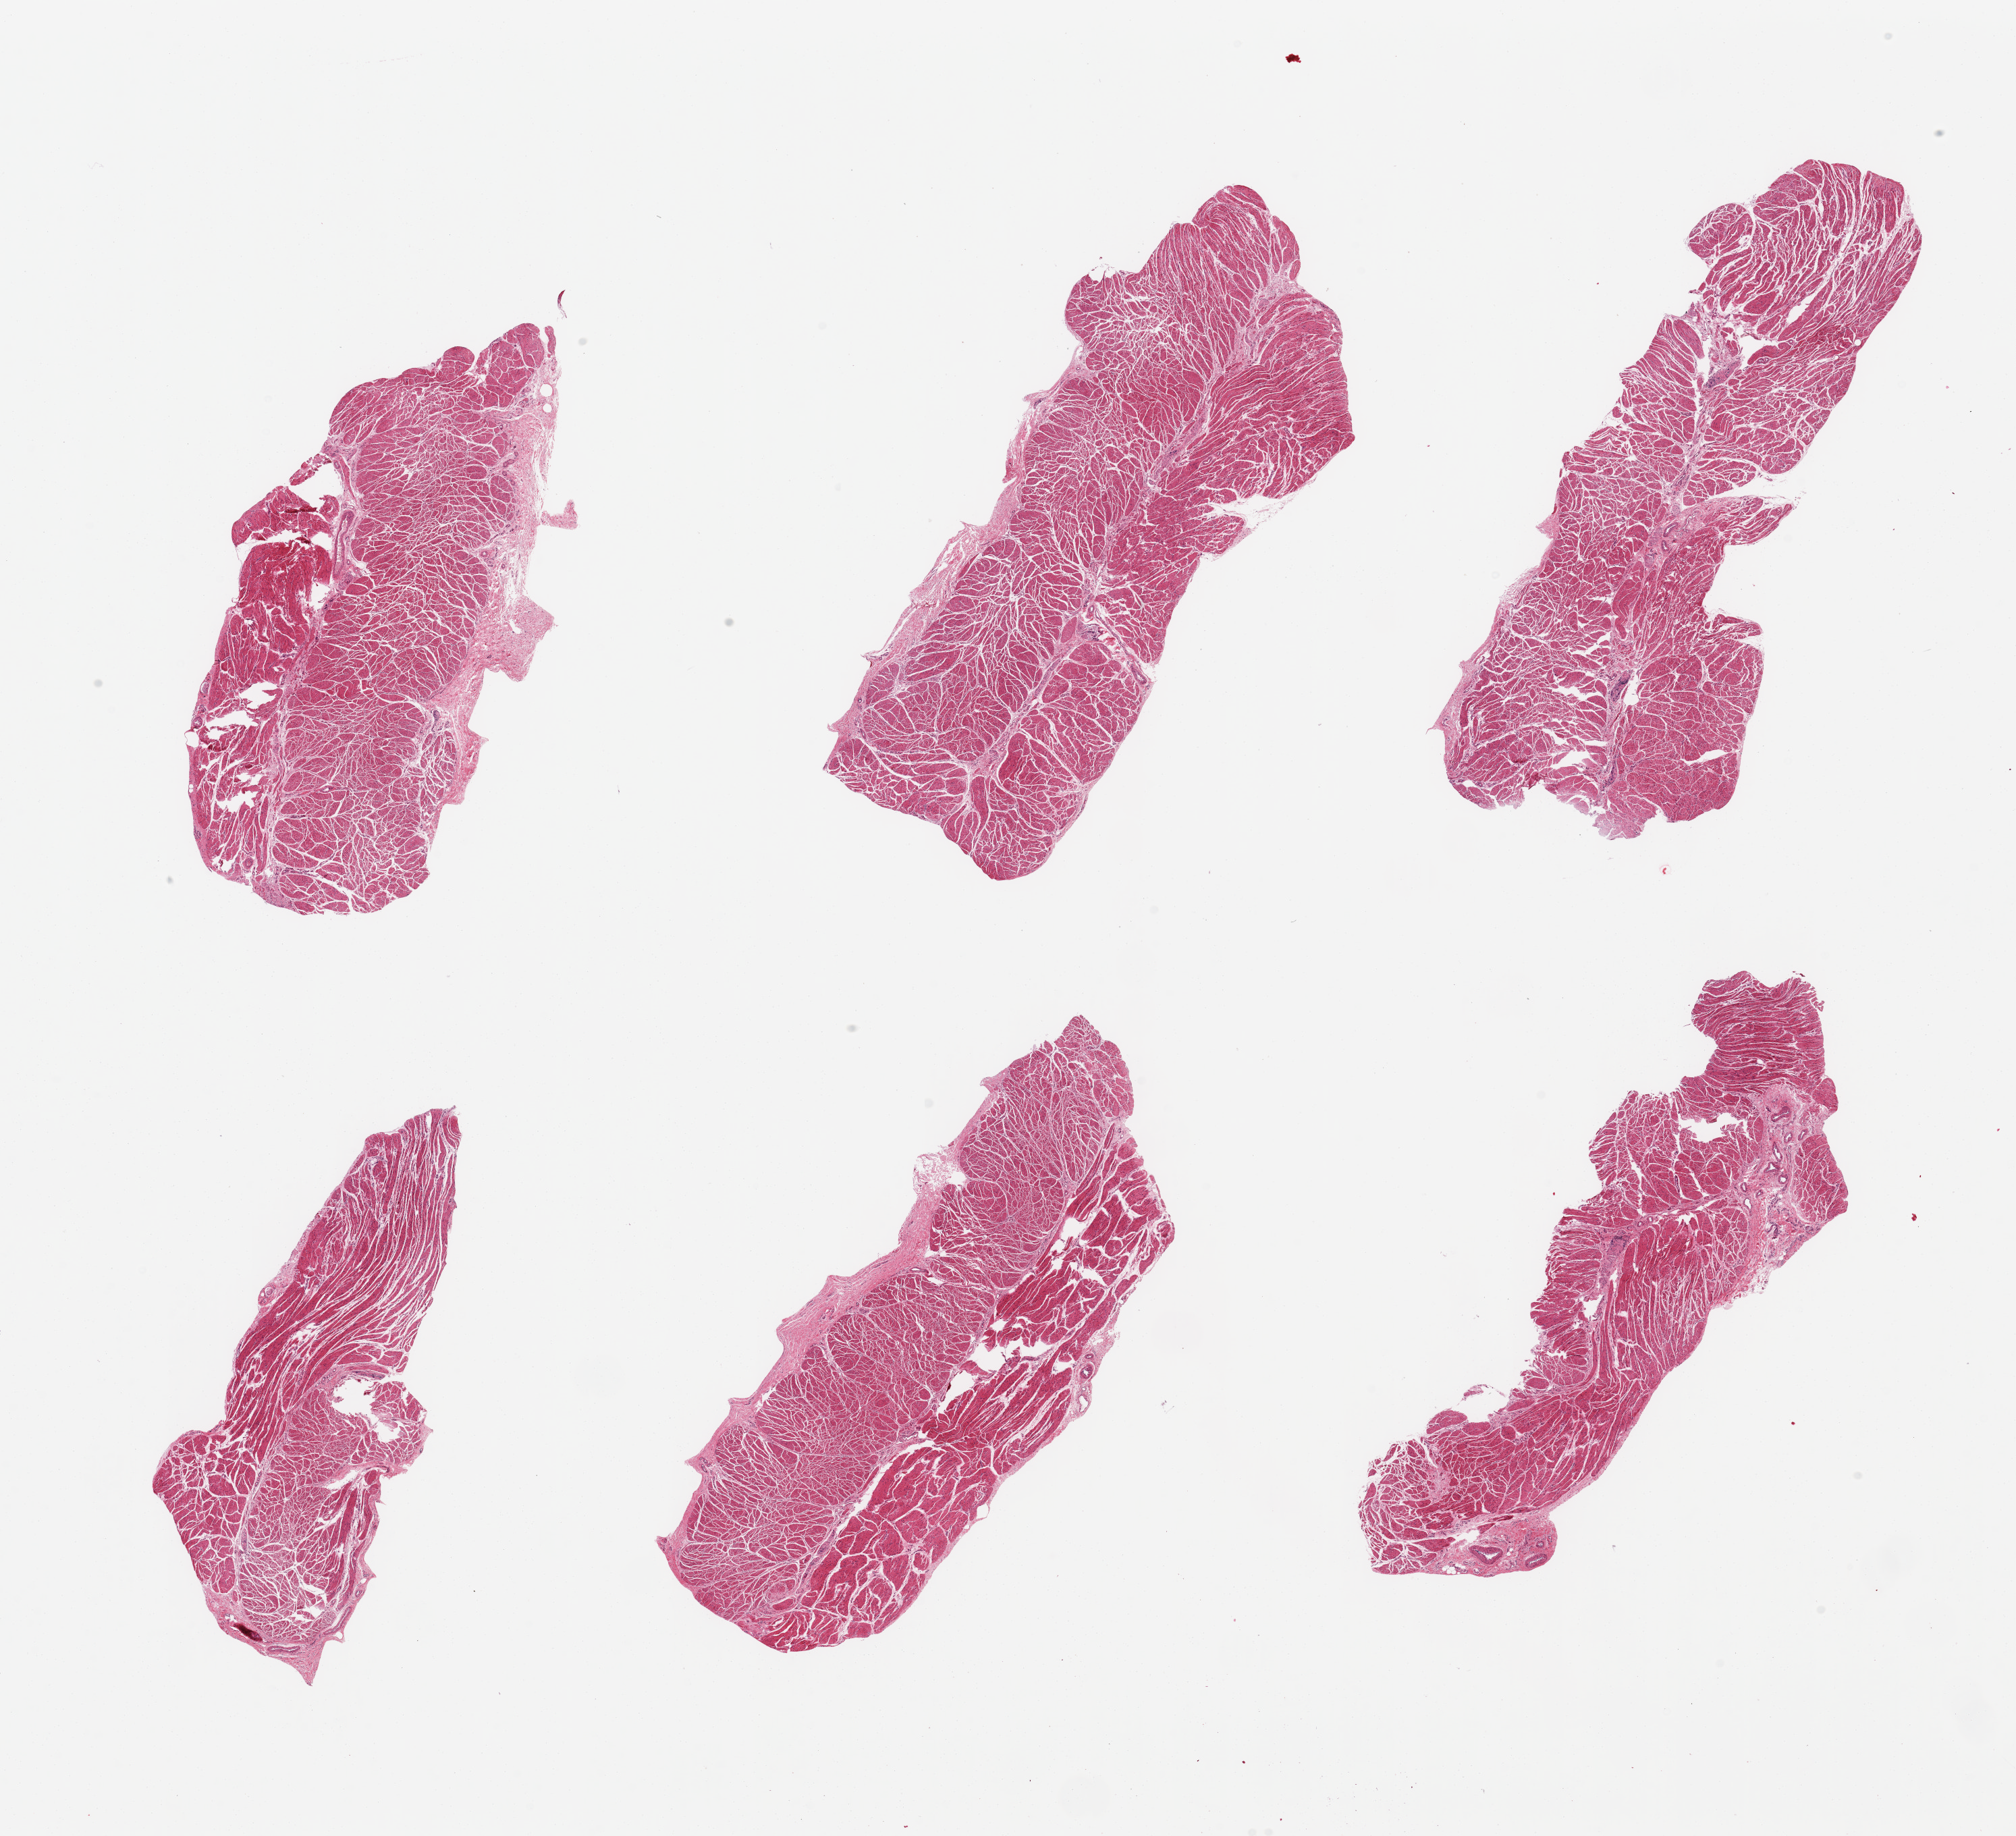
Digitized hematoxylin and eosin (H&E)-stained section, brightfield, shown as a low-resolution overview of the whole scanned area (about 23.6 x 21.5 mm, from a 20x scan), PAXgene-fixed paraffin-embedded (PFPE) section, section of esophageal muscle (target tissue), donor tissue sample. Female donor.
Review note (as recorded): 6 pieces; well trimmed target muscularis.